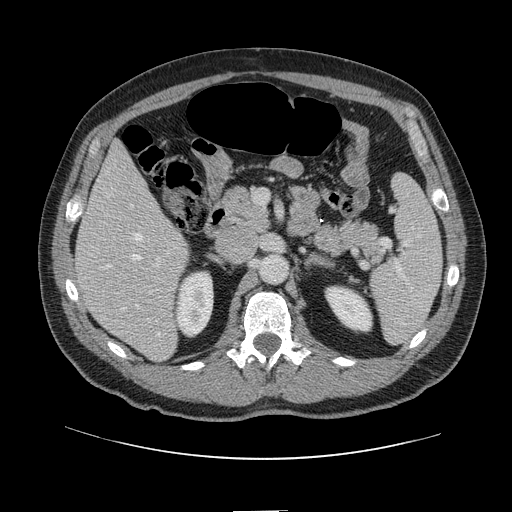
Contrast-enhanced abdominal CT, one axial slice; position 60 of 161 along the scan axis; 120 kVp; intravenous contrast given; soft-tissue window (W 400 / L 40 HU); 2.5 mm slice thickness; 512 × 512 image matrix, field of view 412 × 412 mm. Male patient, age 66 years. From the clinical record (not read from this slice): diagnosis: colorectal cancer liver metastases, imaged before liver resection; multiple liver metastases: no; largest metastasis: 3.5 cm.
Structures marked on this image (expert manual segmentation):
- hepatic veins: box from (x=123, y=233) to (x=160, y=336) px
- liver: (x=76, y=144)–(x=189, y=360)
- planned liver remnant (the part of the liver to remain after resection): (x=76, y=143)–(x=171, y=284)
- portal vein (with intrahepatic branches): (x=149, y=257)–(x=162, y=294)